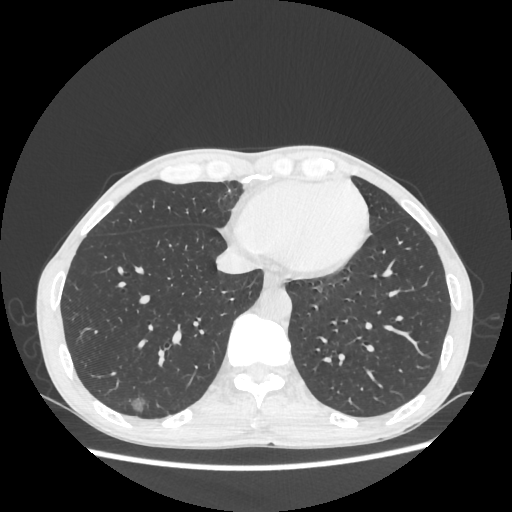
Chest CT, one axial slice; slice 80 of 270 in the series (ordered by position); reconstruction kernel STANDARD; lung window (W 1500 / L -600 HU); 512 × 512 image matrix, field of view 360 × 360 mm. Male patient, age 60 years. Case-level facts recorded for this patient, not image findings: clinical TNM (as recorded): T1c N0 M0; histopathological grade: G2.
Outlined on this slice (bounding box drawn by a radiologist):
- lung tumour (recorded histology: adenocarcinoma): bounding box <120,390,151,423> (left, top, right, bottom; pixels)